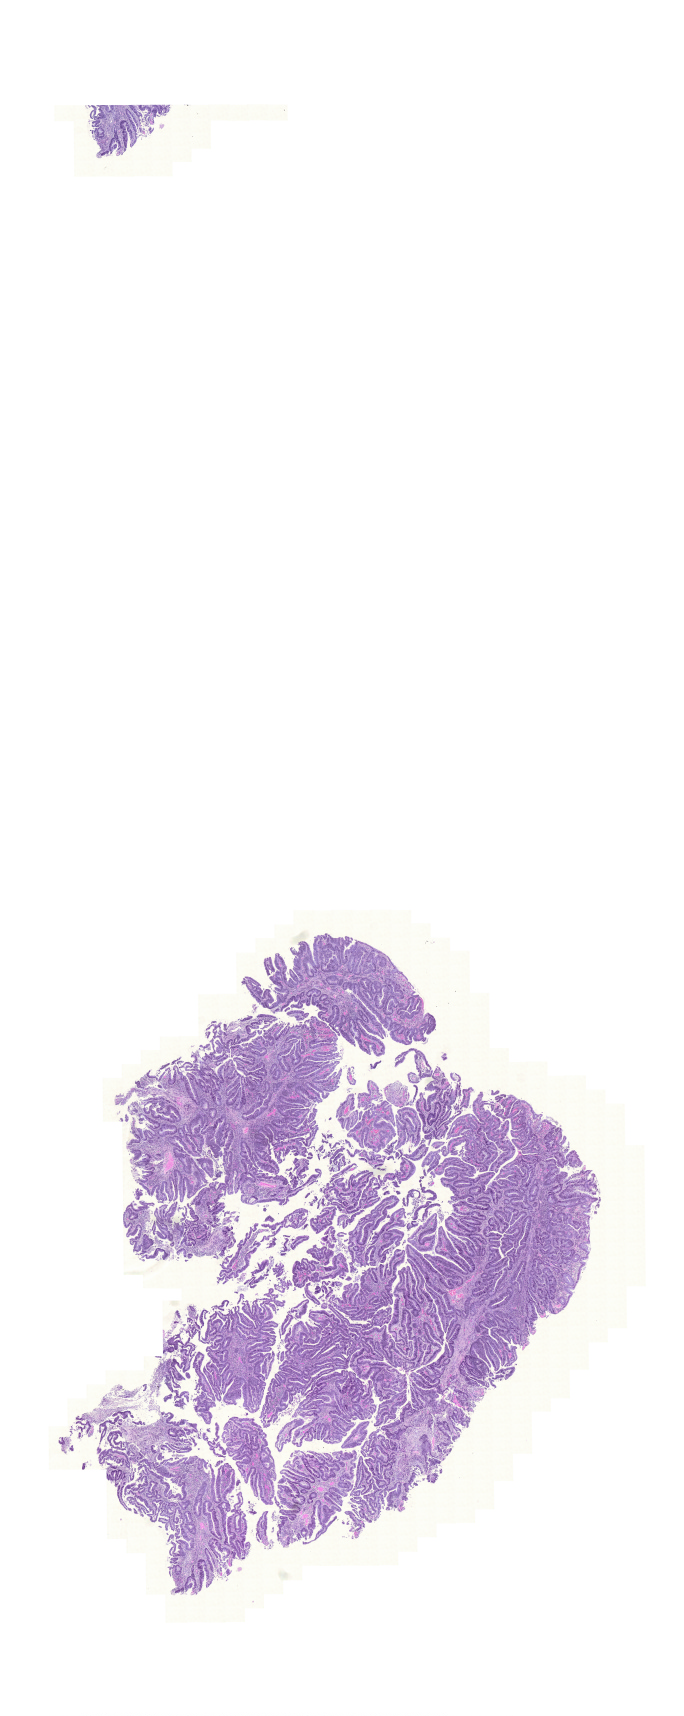
Whole-slide histology image, Hematoxylin and eosin (H&E) stained — whole scanned area (about 10.2 x 25.5 mm) shown as a low-resolution overview. Formalin-fixed paraffin-embedded (FFPE) diagnostic section. Primary tumour sample from the rectum. Patient: male, age at initial diagnosis 68 years.
AJCC pathologic stage: IIIB (6th edition). Pathologic diagnosis: Adenocarcinoma, NOS. Lymph nodes positive (case pathology): 2 of 16 examined.